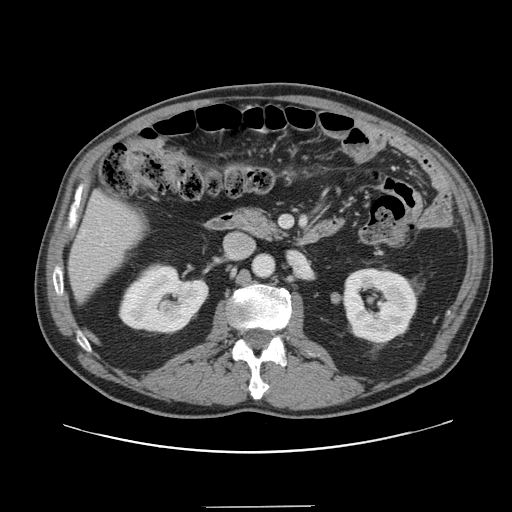
Contrast-enhanced abdominal CT, one axial slice. Slice 60 of 139 in the series (ordered by position). Intravenous contrast given. Soft-tissue window (W 400 / L 40 HU). 2.5 mm slice thickness. 512 × 512 image matrix, field of view 397 × 397 mm. Male patient, age 64 years. Case-level facts recorded for this patient, not image findings: diagnosis: colorectal cancer liver metastases, imaged before liver resection; multiple liver metastases: yes; largest metastasis: 3.5 cm; chemotherapy before resection: yes.
Outlined on this slice (expert manual segmentation):
- liver: bounding box <70,194,144,298> (left, top, right, bottom; pixels)
- planned liver remnant (the part of the liver to remain after resection): <70,194,144,298>